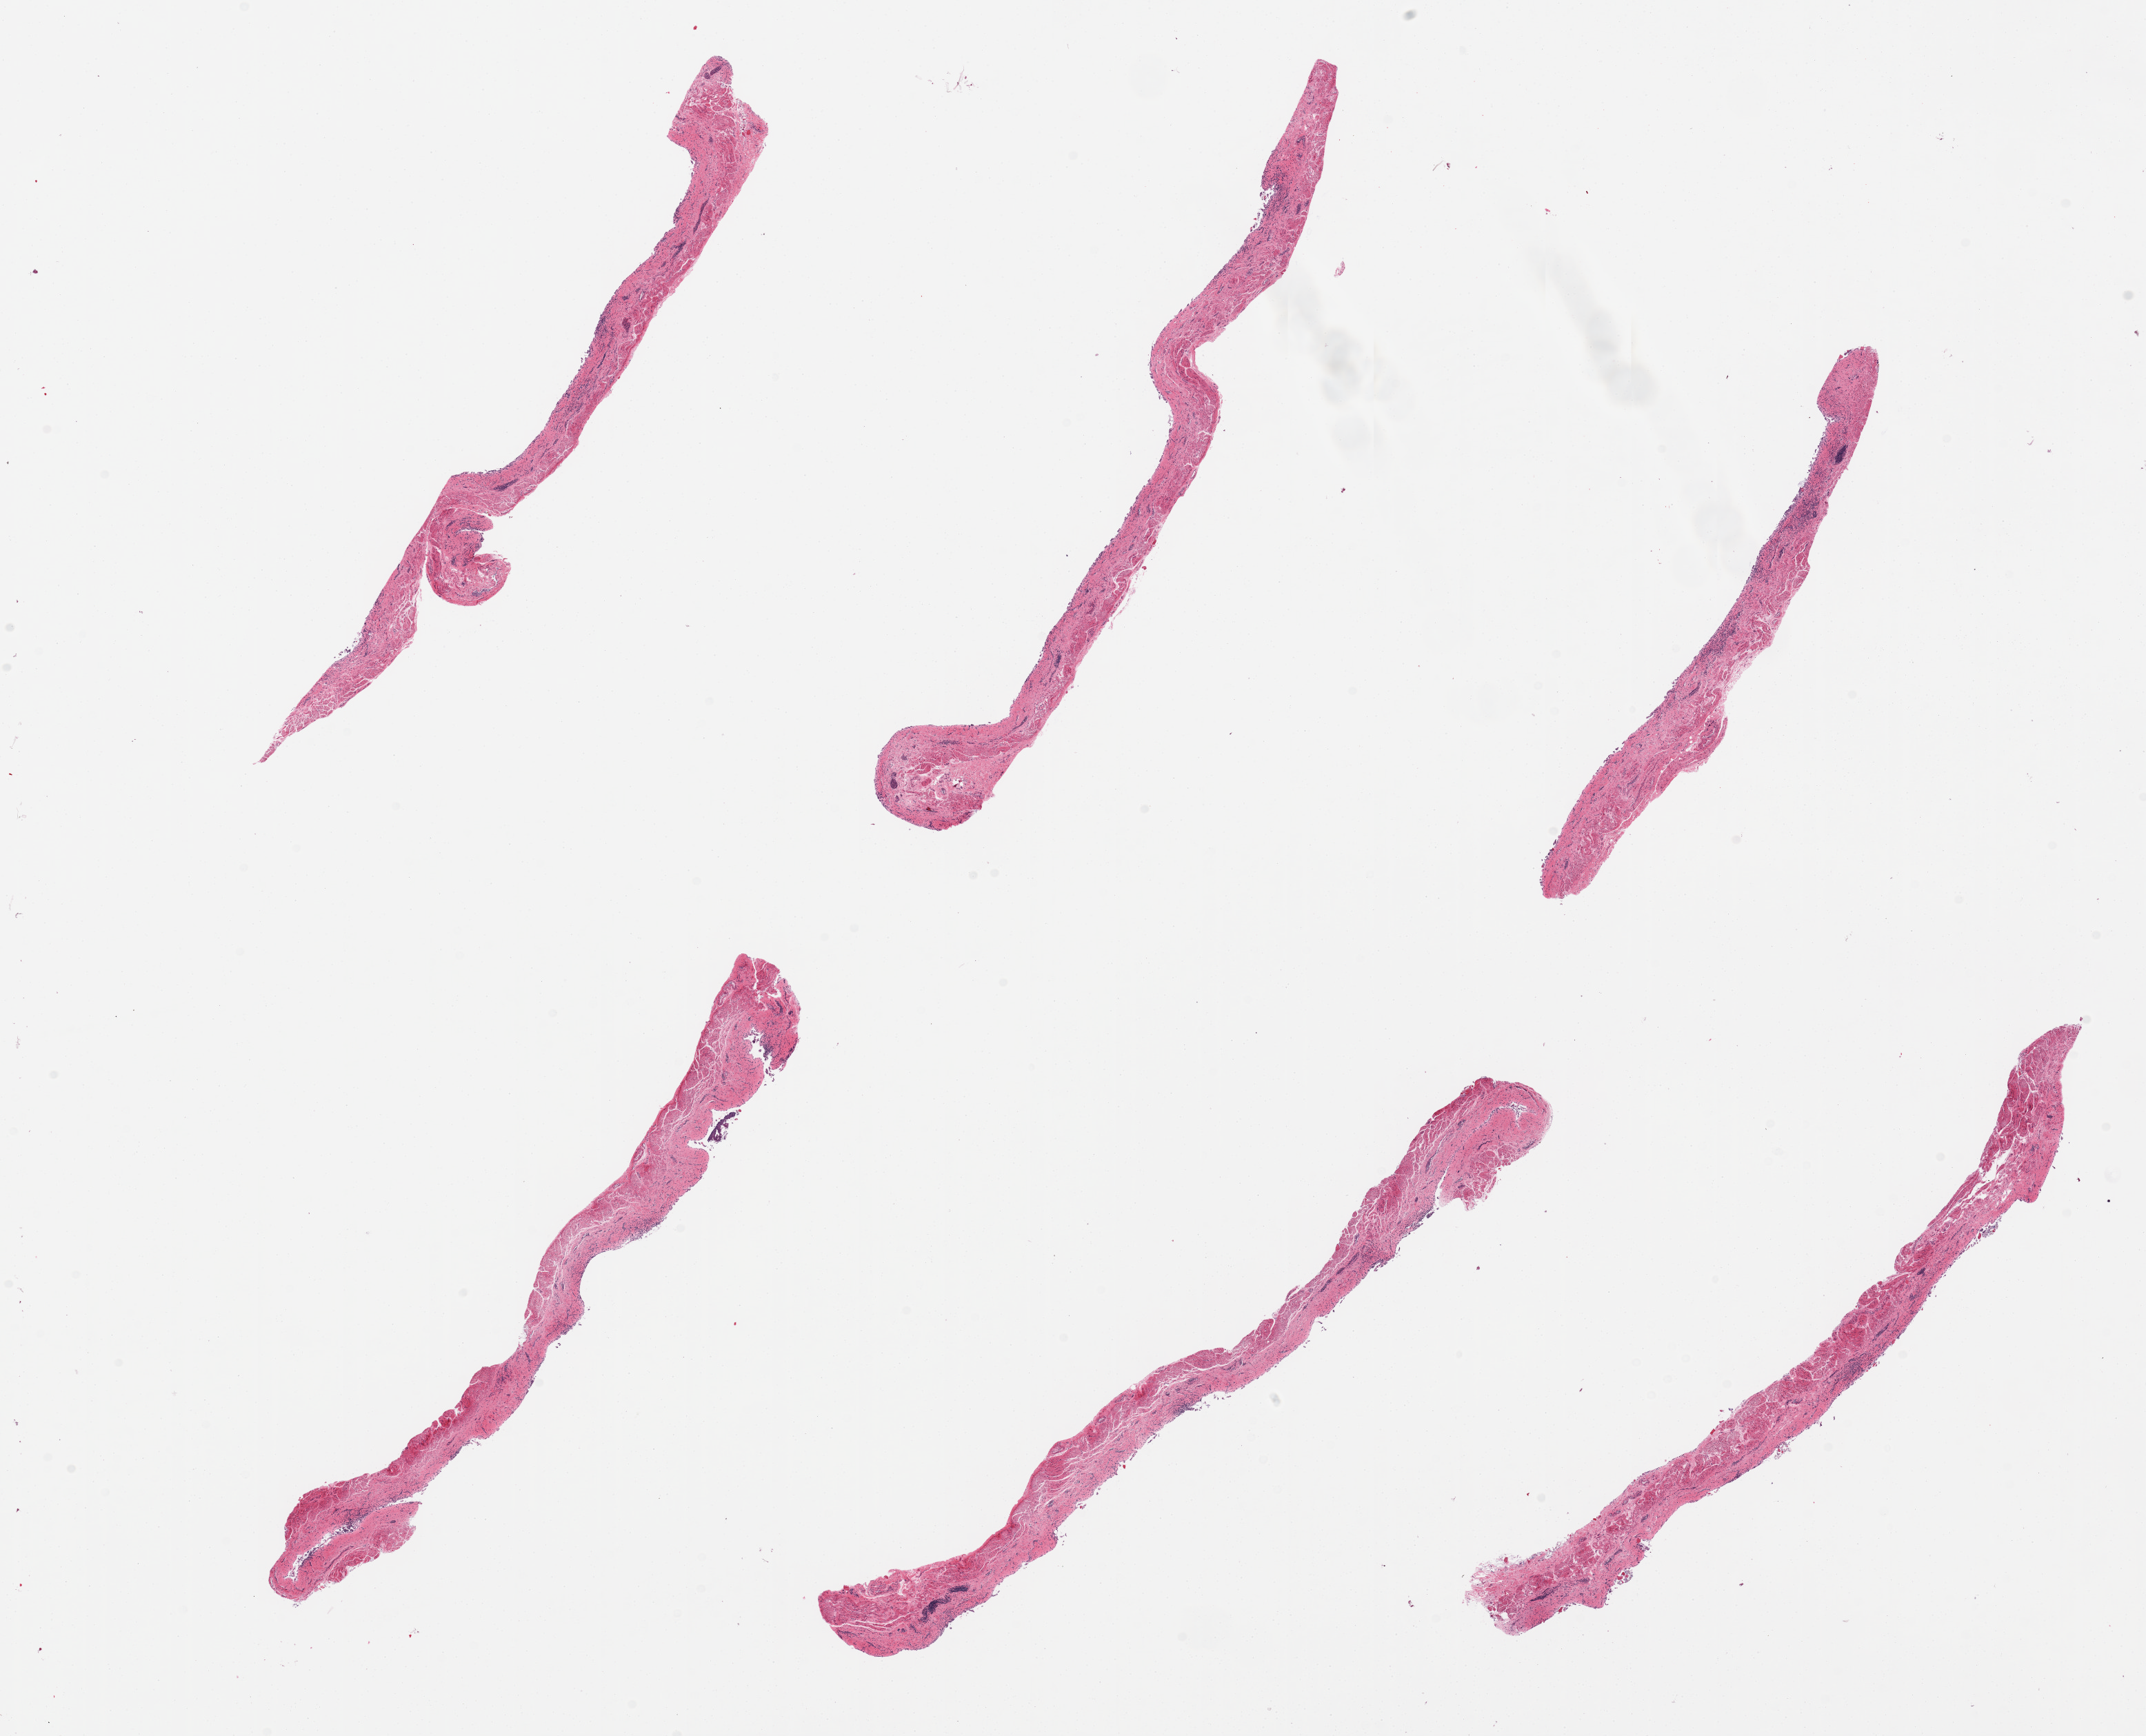
Digitized hematoxylin and eosin (H&E)-stained section, a low-resolution overview of the entire scanned area, about 24.6 x 19.9 mm (from a 20x scan), PAXgene-fixed, paraffin-embedded tissue, target tissue: esophageal mucous membrane, tissue donor sample.
Reviewer comment on this tissue sample: 6 pieces; epithelium totally sloughed.